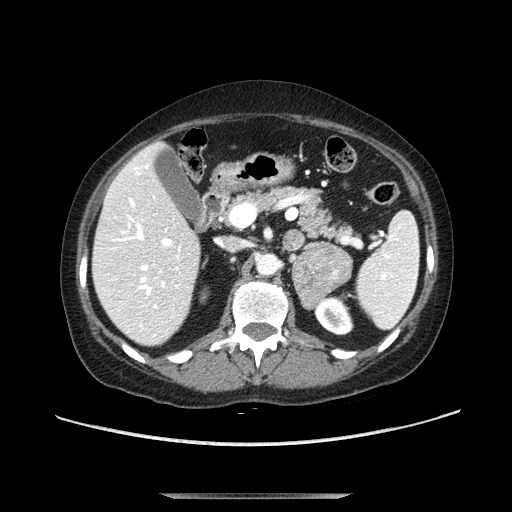
Contrast-enhanced abdominal CT, one axial slice. Slice 61 of 107 in the series (ordered by position). Soft-tissue window (W 400 / L 40 HU). 2.5 mm slice thickness. 512 × 512 image matrix, field of view 380 × 380 mm. Female patient. Case-level facts recorded for this patient, not image findings: diagnosis: adrenocortical carcinoma; tumour side: left adrenal; tumour size at pathology: 7.5 cm; Ki-67 index: 9 %; stage (as recorded): 3.
Annotated regions visible in this slice (semi-automatic segmentation, software-assisted and operator-edited):
- mass: bounding box (x1, y1, x2, y2) in pixels: (292, 244, 353, 308)